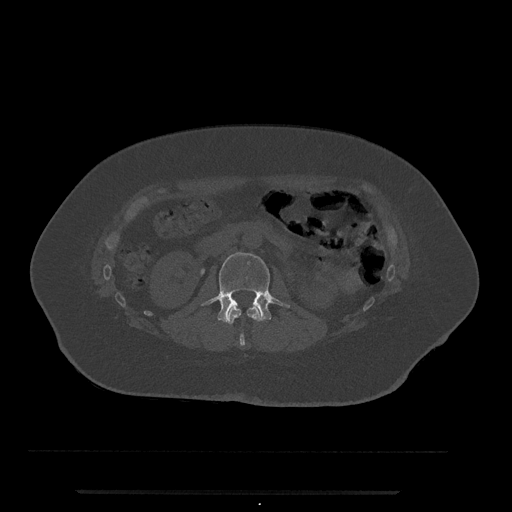
CT including the spine, one axial slice. Slice 55 of 797 in the series (ordered by position). 120 kVp. Bone window (W 1800 / L 400 HU). 0.5 mm slice thickness. 512 × 512 image matrix. Patient: female, 51 years. Case-level facts recorded for this patient, not image findings: primary cancer: neuro.
Annotated regions visible in this slice (semi-automatically segmented with operator editing):
- L1 vertebra: bounding box (x1, y1, x2, y2) in pixels: (226, 307, 262, 346)
- L2 vertebra: (202, 252, 290, 323)